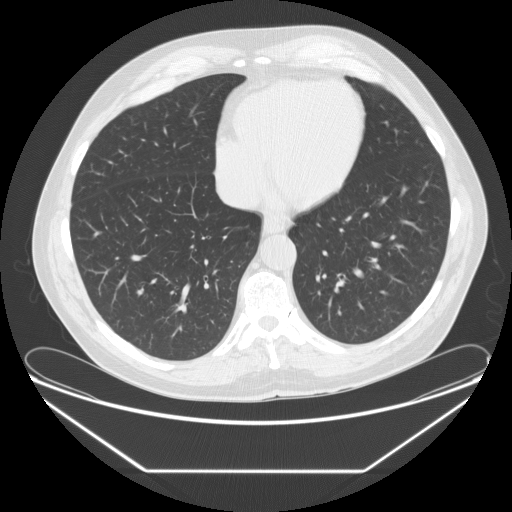
Chest CT (low-dose screening protocol), one axial image, baseline screening round, lung window (W 1500 / L -600 HU), 2.5 mm slice thickness, 512 × 512 image matrix. Male participant, aged 67 years at enrolment. Current smoker at enrolment.
Lesion marked by an expert reader, box from (x=414, y=254) to (x=437, y=281) px. Reader record for this screening exam (exam-level; its link to the box is not recorded): non-calcified nodule or mass ≥4 mm, left lower lobe, 4 × 4 mm, poorly defined margins, soft tissue attenuation. Official screen result: positive, change unspecified: nodule(s) >= 4 mm or enlarging nodule(s), mass(es), or other non-specific abnormalities suspicious for lung cancer.